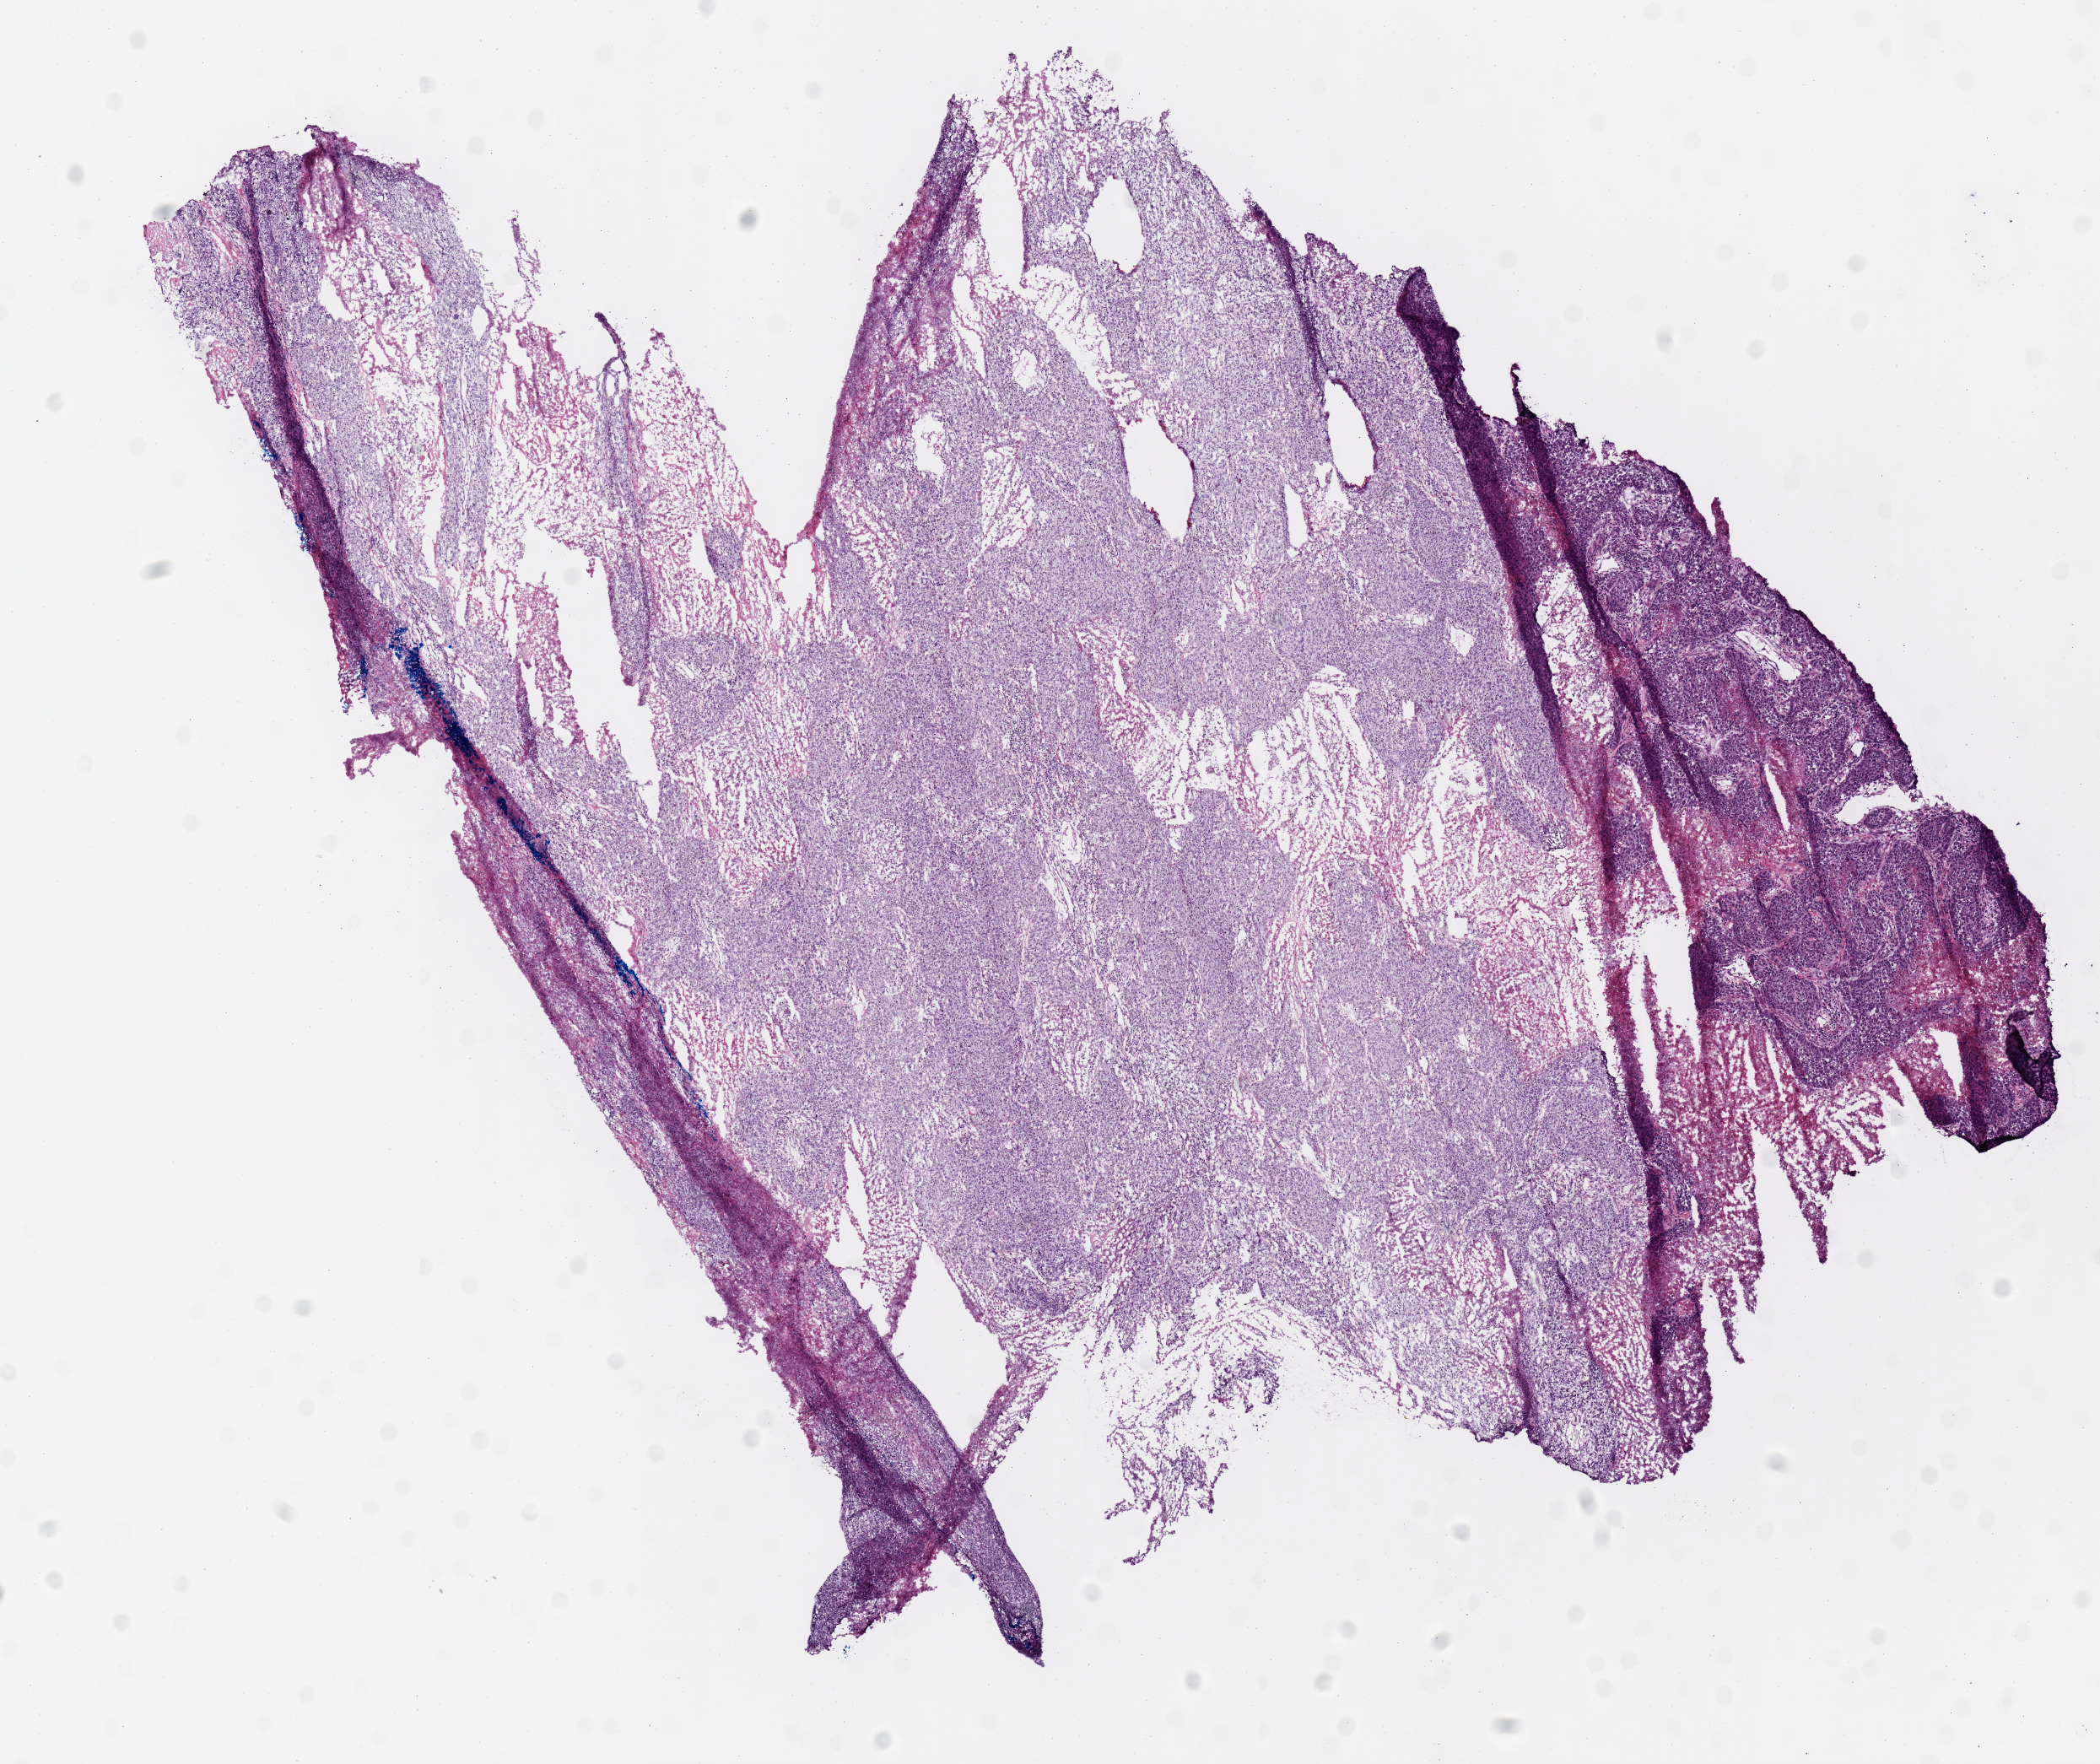
Whole-slide histology image, H&E-stained, shown as a low-resolution overview of the whole scanned area (about 9.8 x 8.3 mm); frozen section; primary tumour sample from the lung. Patient: female, age at initial diagnosis 55 years. Pathologist review of this section (percent, as recorded): tumour cells 80%, tumour nuclei 80%, normal cells 0%, stromal cells 0%, necrosis 20%. Inflammatory infiltration, as recorded: lymphocyte infiltration 10%, monocyte infiltration 0%, neutrophil infiltration 5%.
Laterality: right. AJCC pathologic stage: IIB (7th edition). Pathologic diagnosis: Squamous cell carcinoma, NOS (lower lobe, lung).